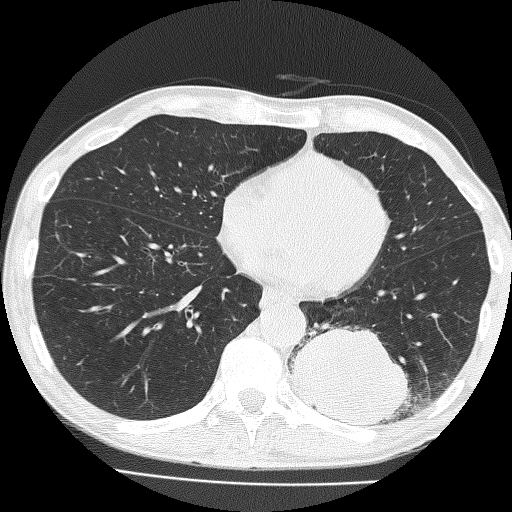
Low-dose screening chest CT, one axial slice; slice 63 of 160 in the series (ordered by position); reconstruction kernel FC51; 120 kVp; lung window (W 1500 / L -600 HU); 2 mm slice thickness; 512 × 512 image matrix.
Outlined on this slice (outlined manually by an expert reader):
- lesion 1 (tumor, lower lobe of left lung): box from (x=290, y=326) to (x=410, y=425) px